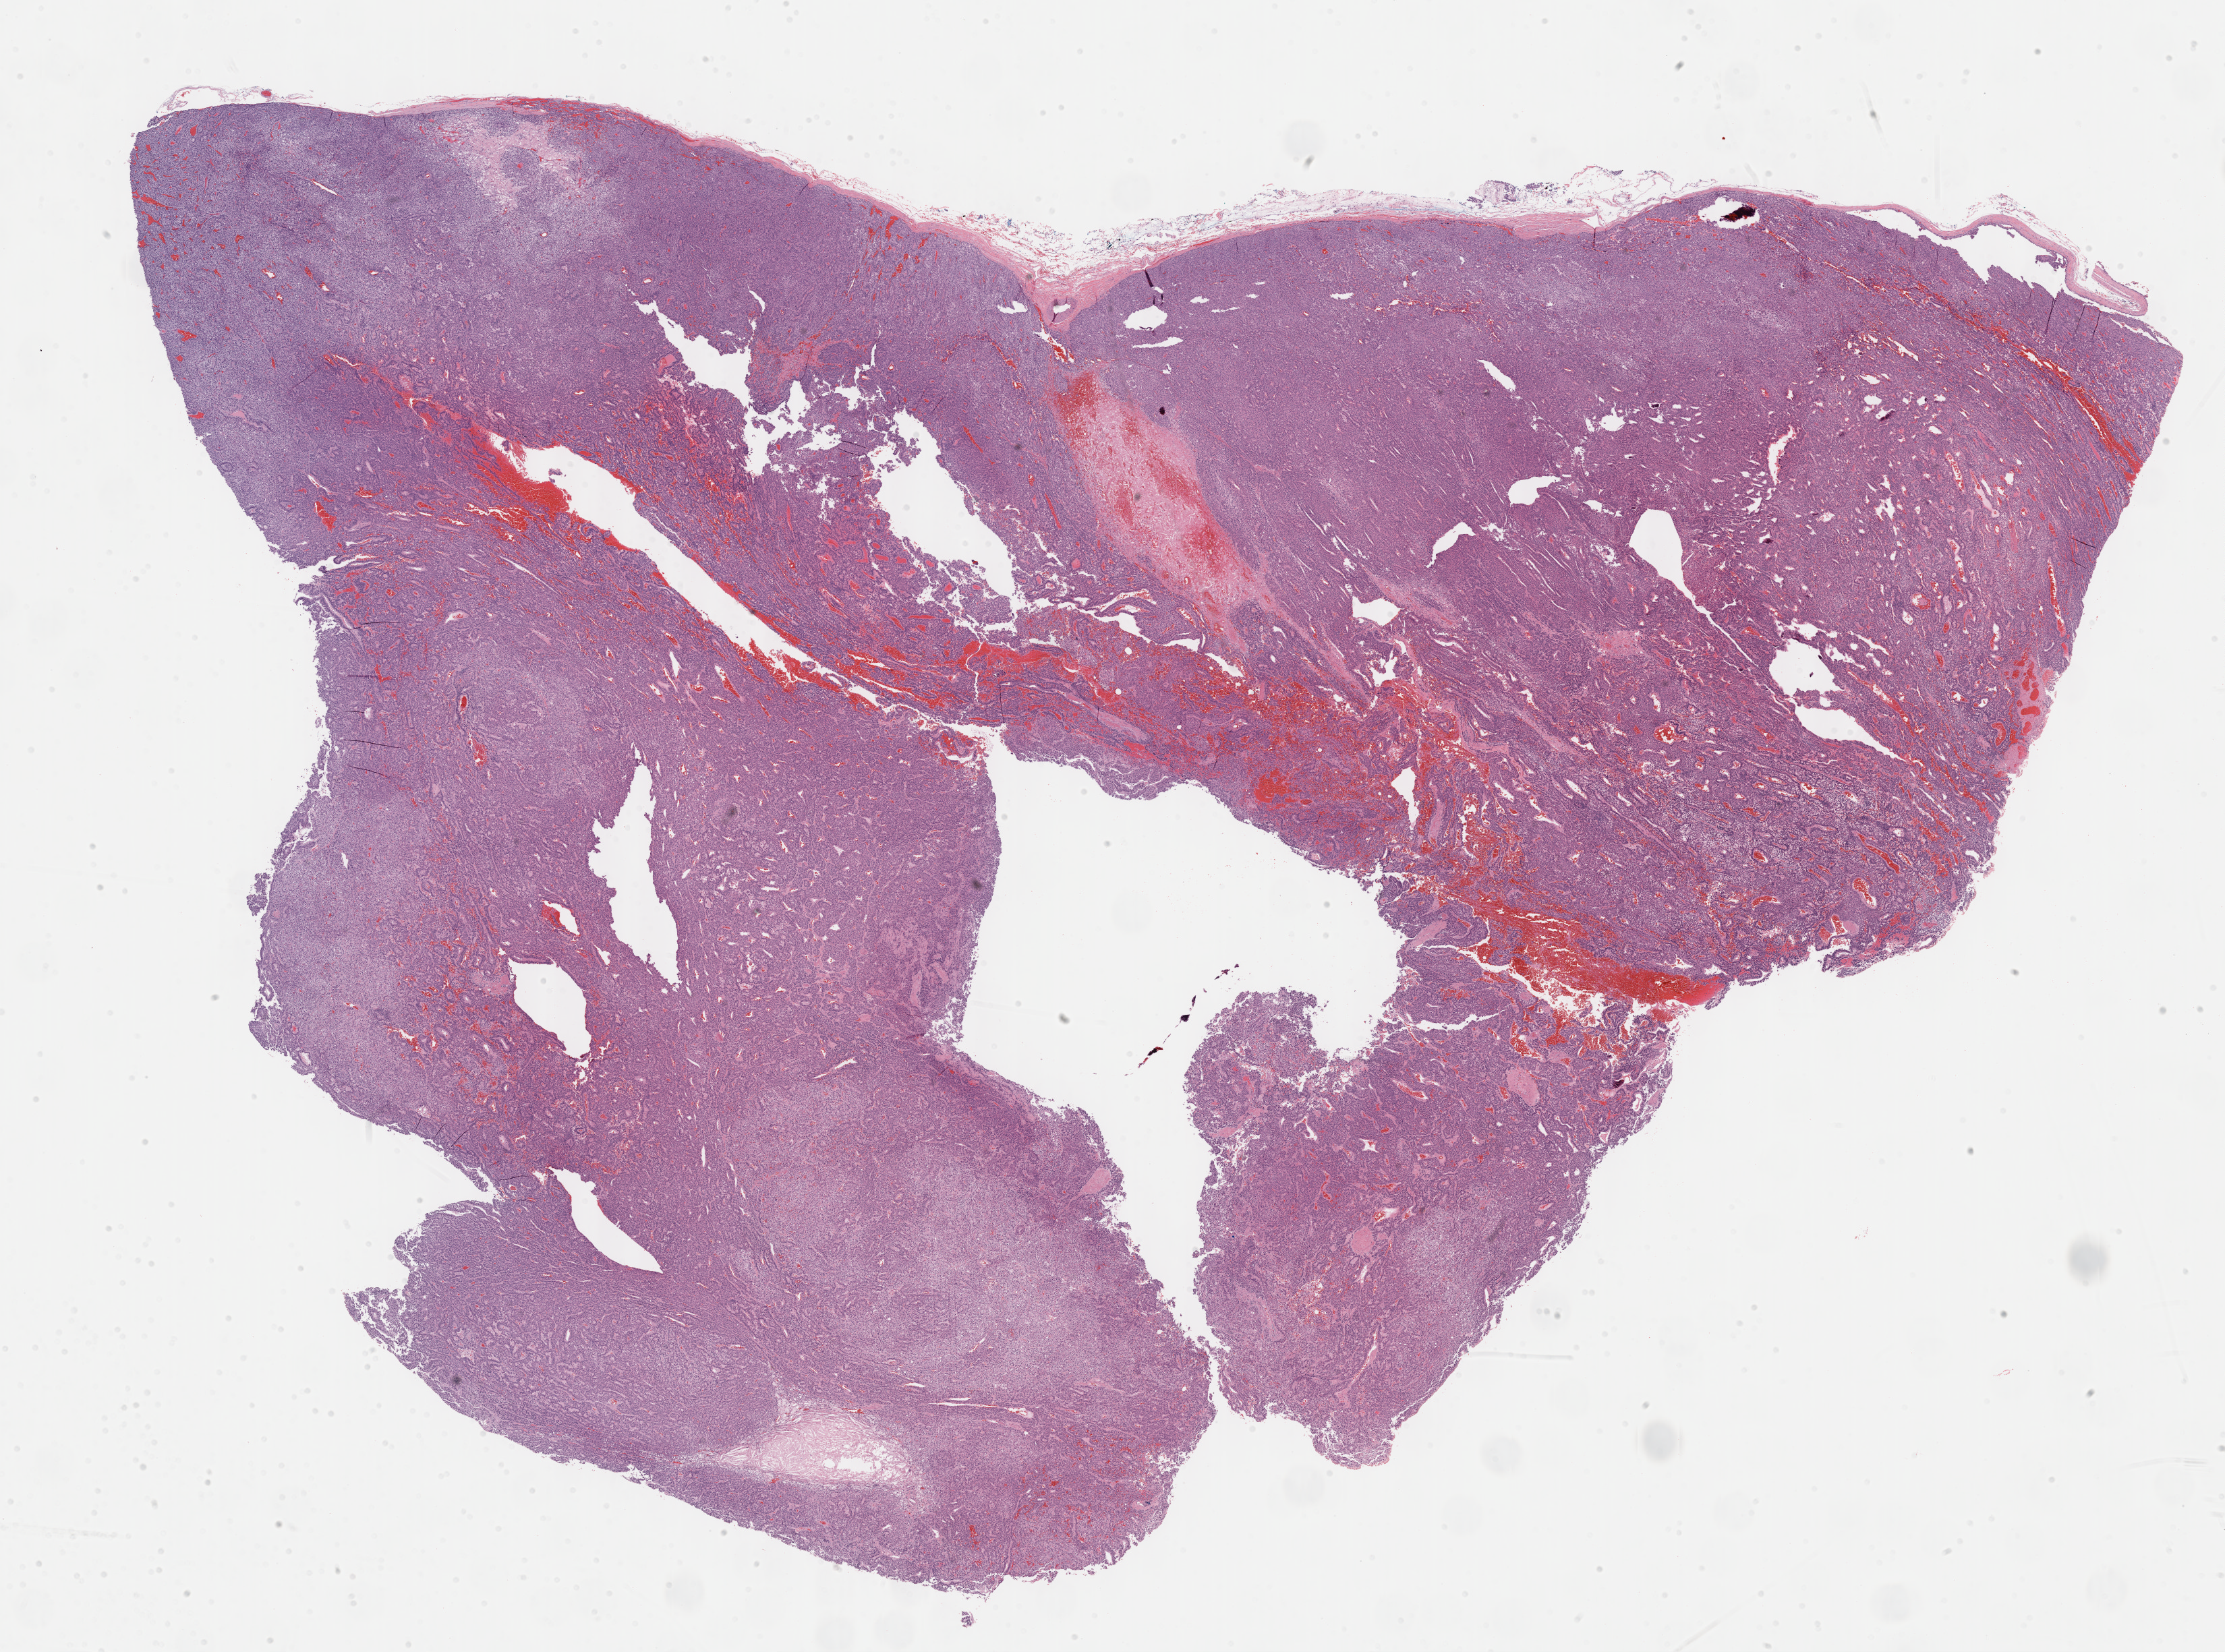
Whole-slide histology image, Hematoxylin and eosin (H&E) stained, a low-resolution overview of the entire scanned area, about 26.7 x 19.8 mm (acquisition: 40x scan), FFPE section, adrenal cortex, primary tumour sample. Female patient; age at initial diagnosis 69 years.
- laterality: left
- pathologic diagnosis: Adrenal cortical carcinoma (cortex of adrenal gland)